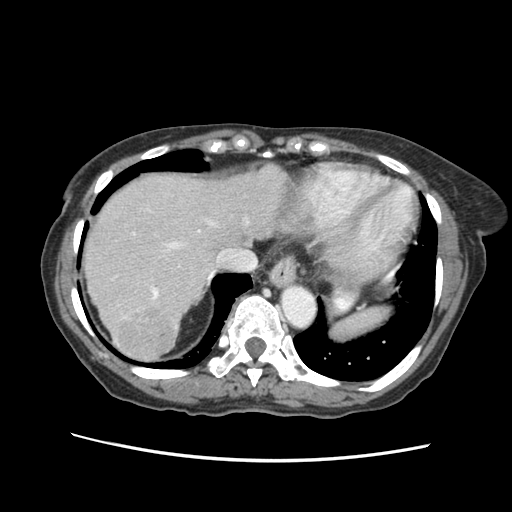
Contrast-enhanced abdominal CT (liver protocol), one axial slice; position 49 of 63 along the scan axis; reconstruction kernel STANDARD; soft-tissue window (W 400 / L 40 HU); 2.5 mm slice thickness; 512 × 512 image matrix. From the clinical record (not read from this slice): diagnosis: hepatocellular carcinoma (patient treated with transarterial chemoembolisation; whether this scan precedes or follows treatment is not stated here); TNM stage (as recorded): Stage-I; Child-Pugh class: B; tumour differentiation: well differentiated.
Annotated regions visible in this slice (semi-automatic segmentation, software-assisted and operator-edited):
- liver parenchyma outside the tumour (the mass and vessels are separate outlines, so this box may not span the whole liver): box from (x=82, y=162) to (x=302, y=360) px
- mass: (x=113, y=307)–(x=175, y=358)
- liver vessels: (x=144, y=207)–(x=244, y=299)